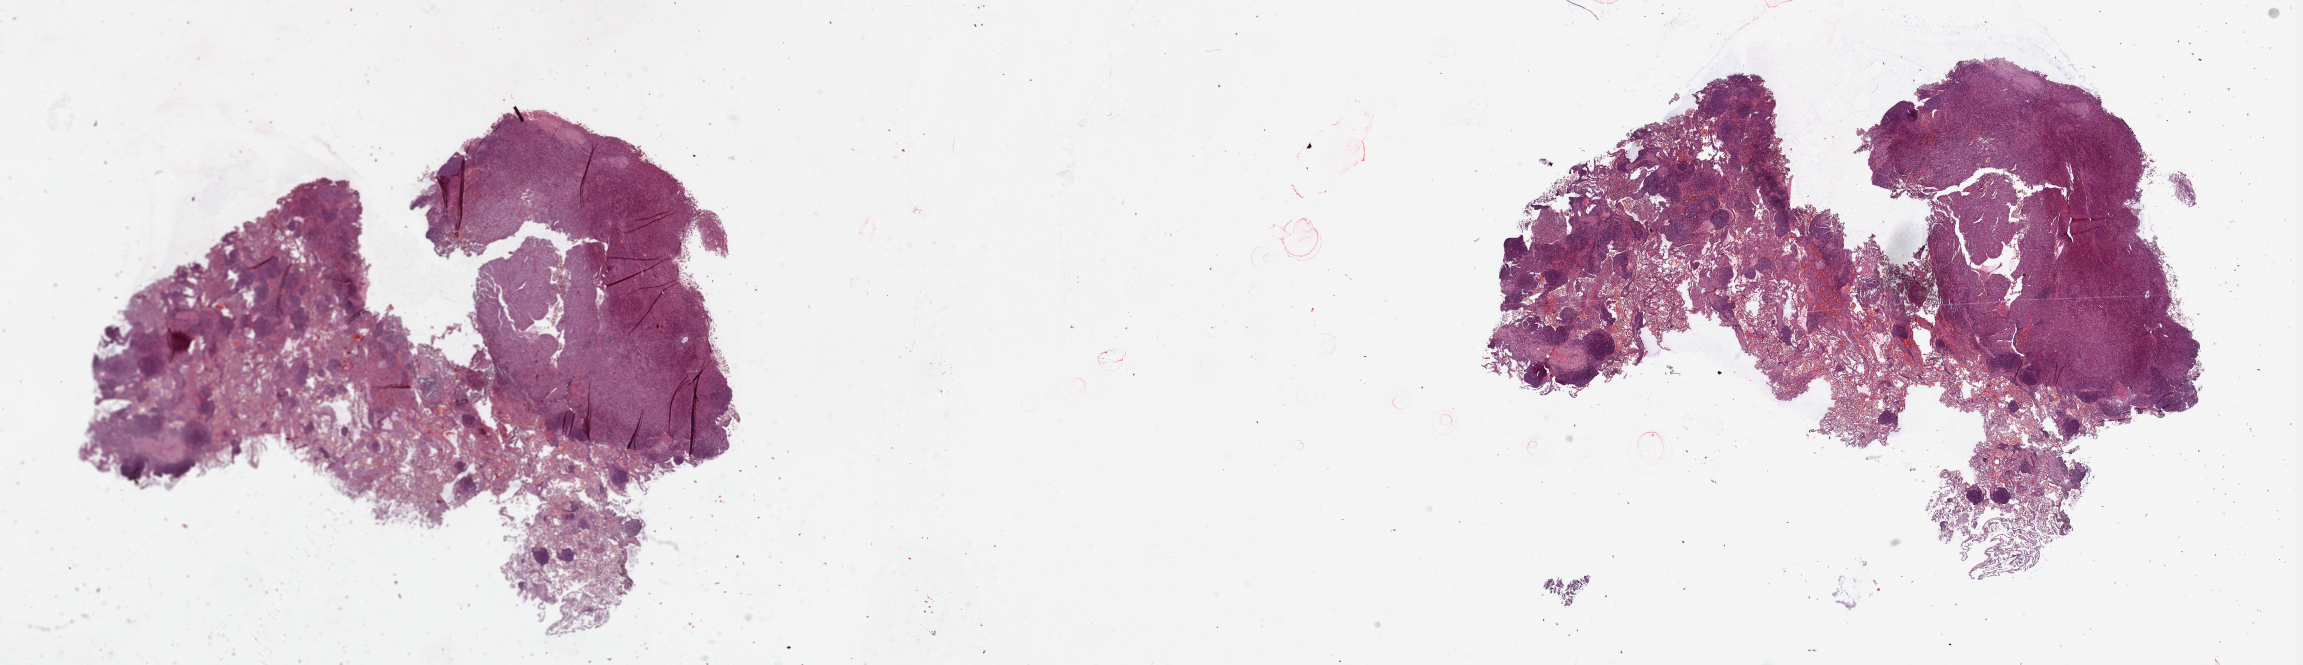
Whole-slide histology image, Hematoxylin and eosin (H&E) stained — a low-resolution overview of the entire scanned area, about 36.4 x 10.5 mm (from a 20x scan); lung, tumour tissue. 56-year-old male patient. Histologic grade: G3 (poorly differentiated).
* AJCC pathologic stage: IIA
* diagnosis: Adenocarcinoma, NOS